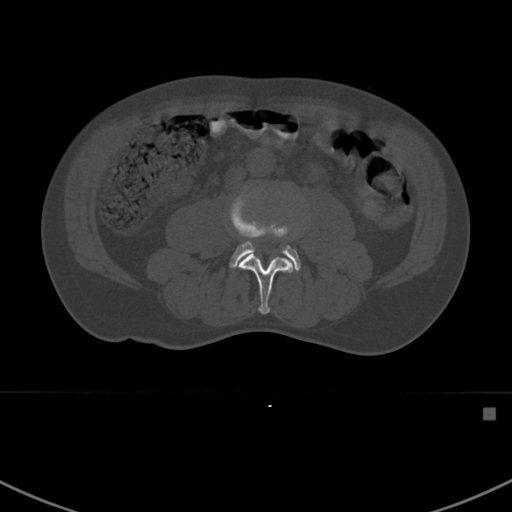
CT including the spine, one axial slice; position 254 of 412 along the scan axis; bone window (W 1800 / L 400 HU); 512 × 512 image matrix, field of view 358 × 358 mm. Patient: male, 59 years. Case-level facts recorded for this patient, not image findings: primary cancer: prostate.
Annotated regions visible in this slice (semi-automatic segmentation, software-assisted and operator-edited):
- L3 vertebra: bounding box [x1, y1, x2, y2] px = [236, 253, 294, 314]
- L4 vertebra: [230, 193, 301, 271]